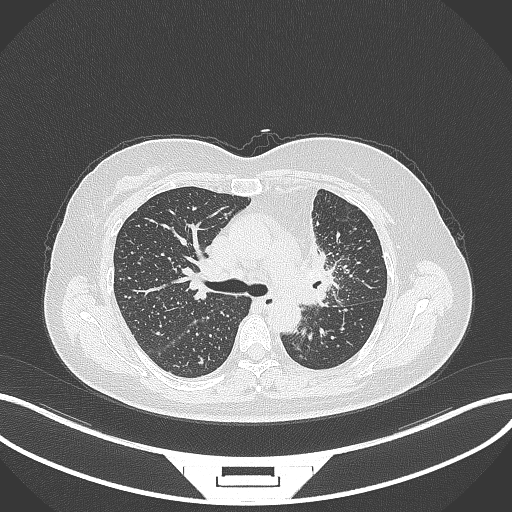
Chest CT, one axial slice. Slice 214 of 348 in the series (ordered by position). Lung window (W 1500 / L -600 HU). 1 mm slice thickness. 512 × 512 image matrix, field of view 400 × 400 mm. Female patient, age 49 years. Case-level facts recorded for this patient, not image findings: clinical TNM (as recorded): T1c N0 M1.
Annotated regions visible in this slice (rectangle marked by the reading radiologist):
- lung tumour (recorded histology: adenocarcinoma): bounding box (x1, y1, x2, y2) in pixels: (294, 238, 341, 308)